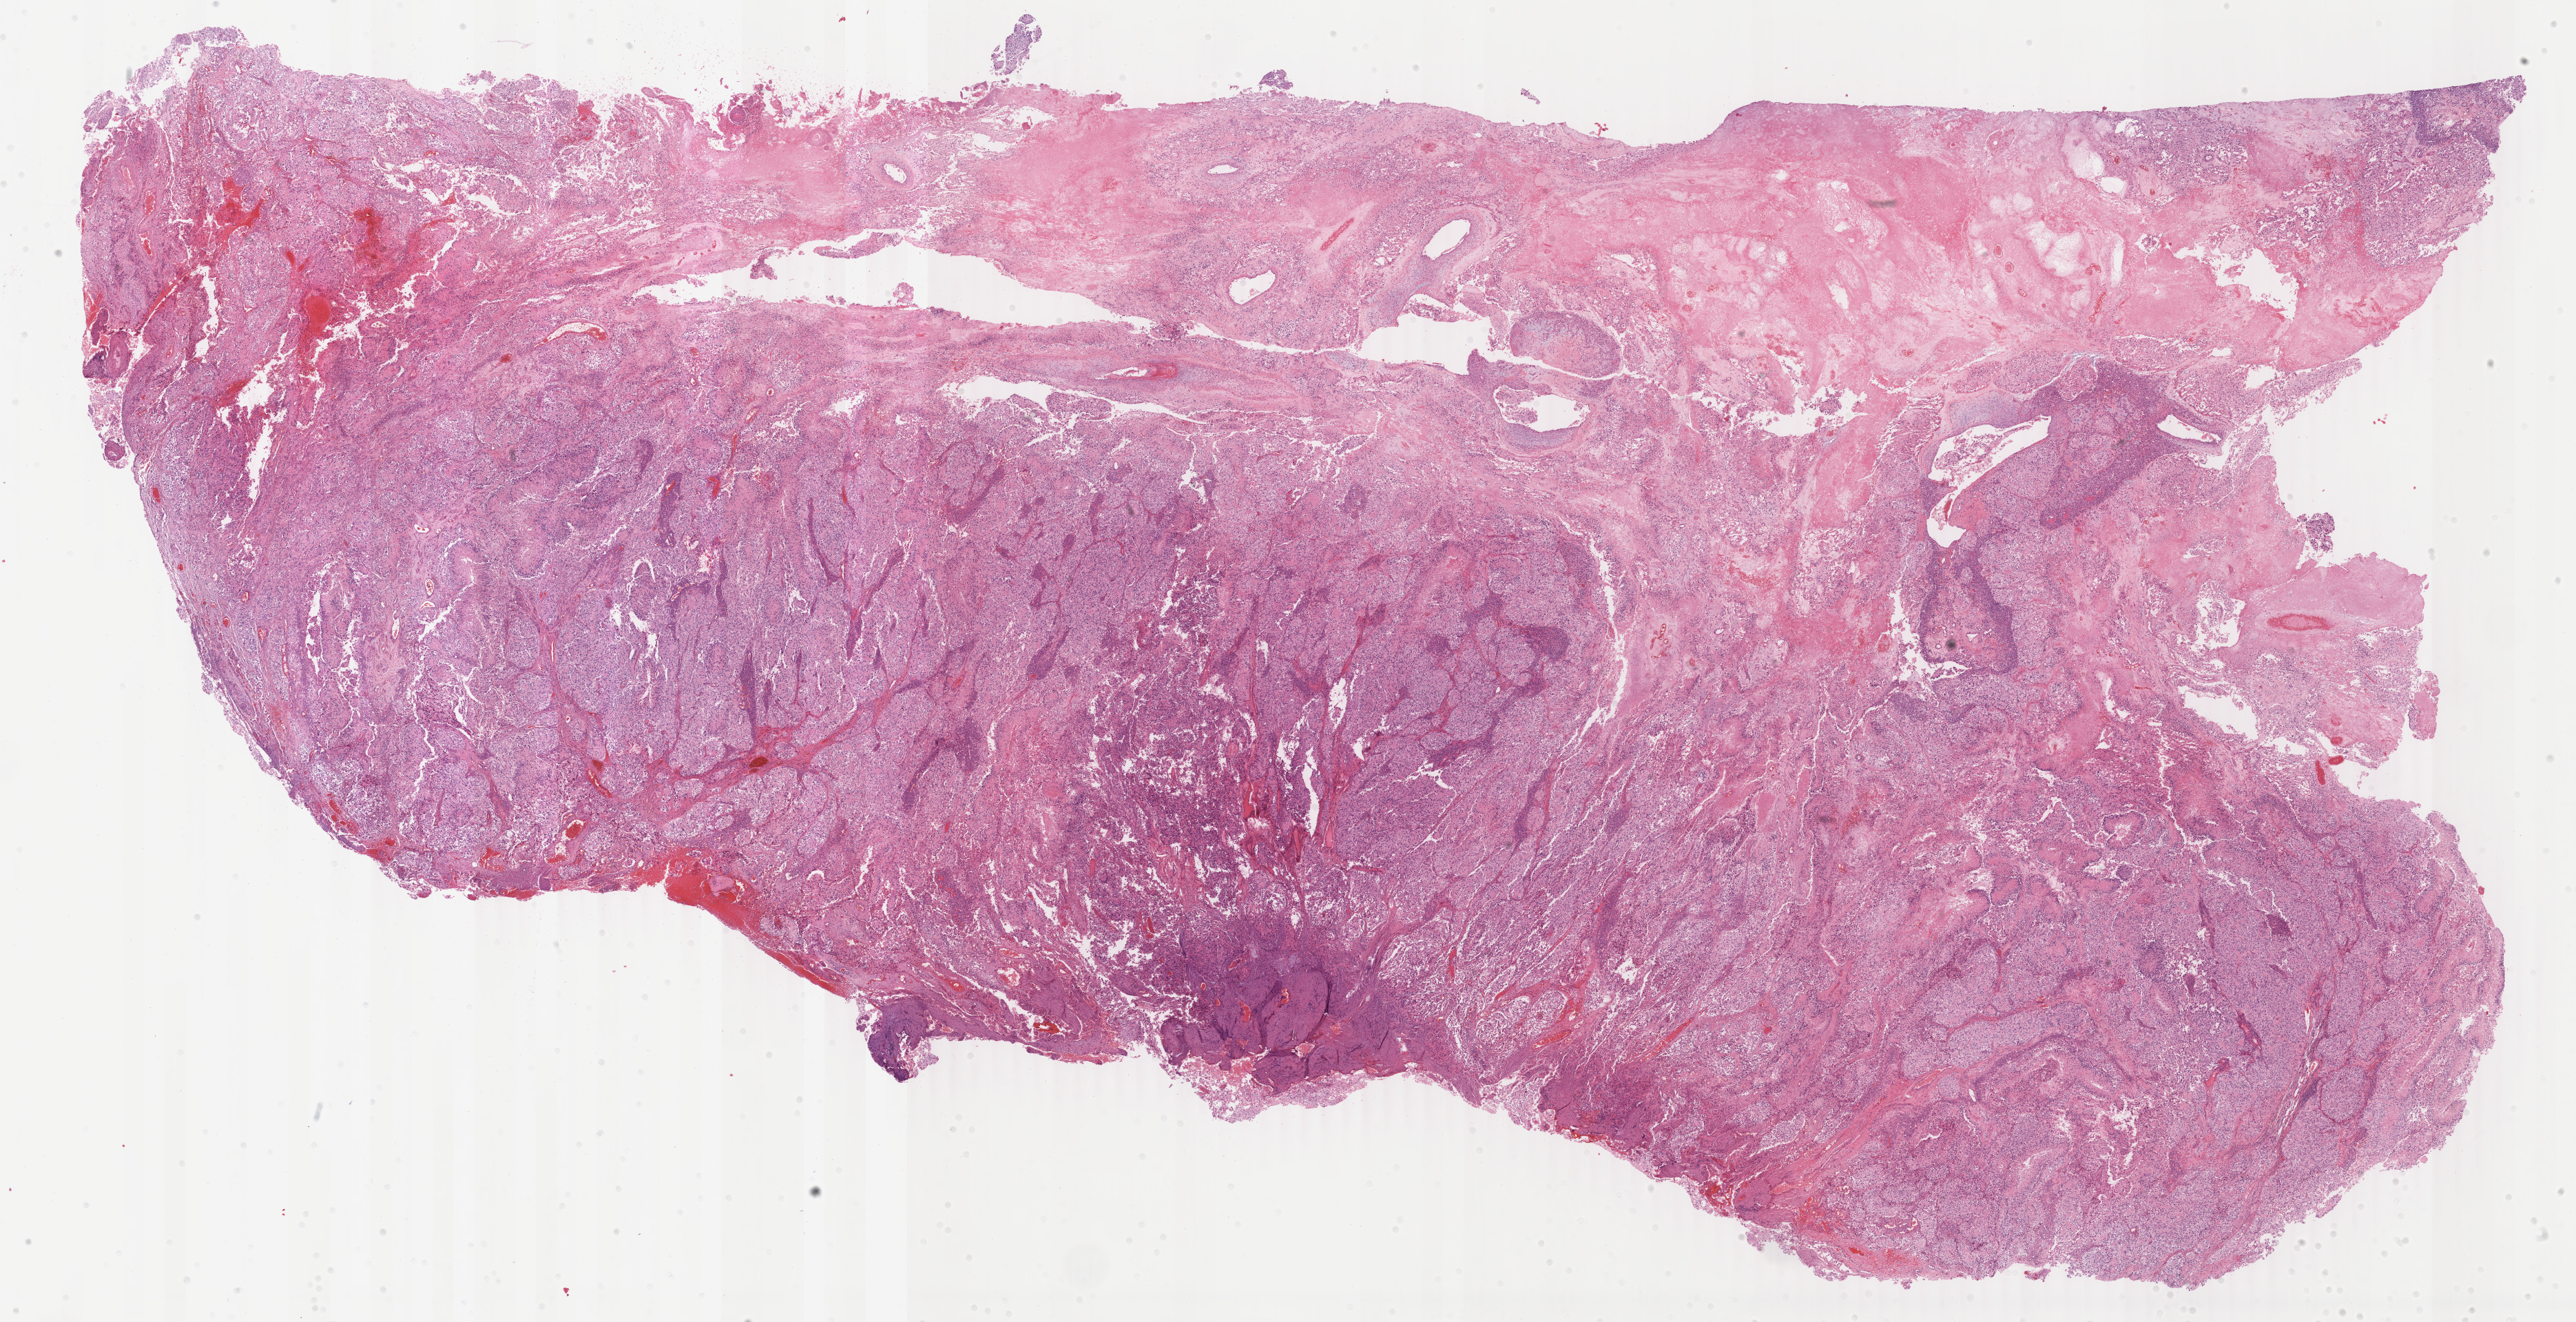
Whole-slide histology image, H&E, shown as a low-resolution overview of the whole scanned area (about 29.7 x 15.3 mm), FFPE section, sample: primary tumour, brain. Male patient; age at initial diagnosis 57 years.
Diagnosis: Glioblastoma.